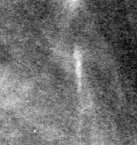
Region of interest cut from a scanned film mammogram (one marked finding), left breast, MLO view, BI-RADS breast density category 2 (scale 1–4).
Marked abnormality: calcifications, morphology fine linear branching, distribution clustered / linear; BI-RADS assessment category 4; subtlety rating 3 on a 1 (subtle) to 5 (obvious) scale; pathology result (as recorded, not read from the image): malignant.